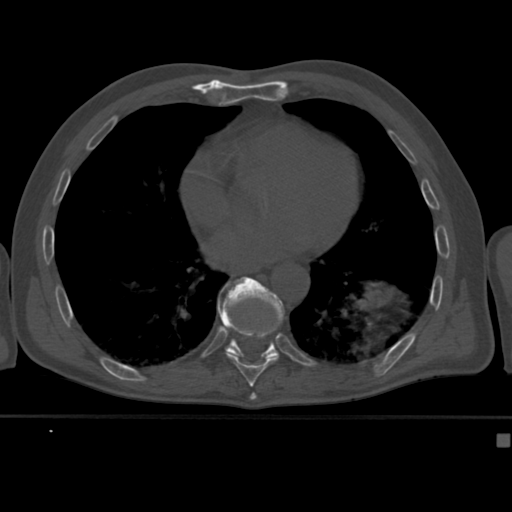
CT including the spine, one axial slice. Position 240 of 430 along the scan axis. Bone window (W 1800 / L 400 HU). 1.5 mm slice thickness. 512 × 512 image matrix, field of view 337 × 337 mm. Male patient, age 64 years. From the clinical record (not read from this slice): primary cancer: uterus; vertebrae with lytic lesions (as recorded): T1, T4, T5, T7, L5.
Annotated regions visible in this slice (semi-automatically segmented with operator editing):
- T10 vertebra: bounding box [x1, y1, x2, y2] px = [217, 277, 285, 364]
- T9 vertebra: [218, 286, 278, 382]